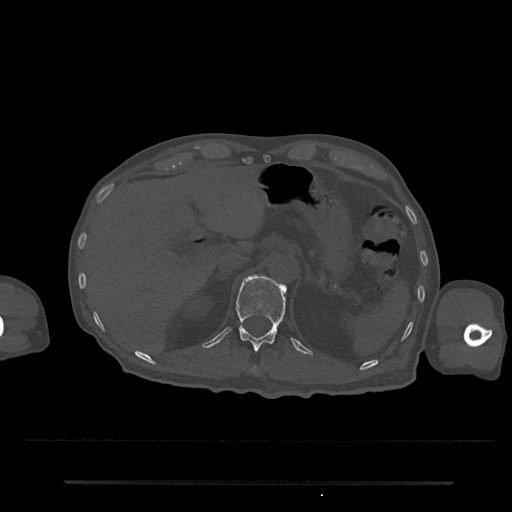
CT including the spine, one axial slice; position 193 of 797 along the scan axis; bone window (W 1800 / L 400 HU); 0.5 mm slice thickness; 512 × 512 image matrix, field of view 427 × 427 mm. Male patient, age 74 years. From the clinical record (not read from this slice): primary cancer: prostate.
Annotated regions visible in this slice (semi-automatically segmented with operator editing):
- T11 vertebra: bounding box [x1, y1, x2, y2] px = [252, 366, 258, 372]
- T12 vertebra: [236, 276, 286, 352]